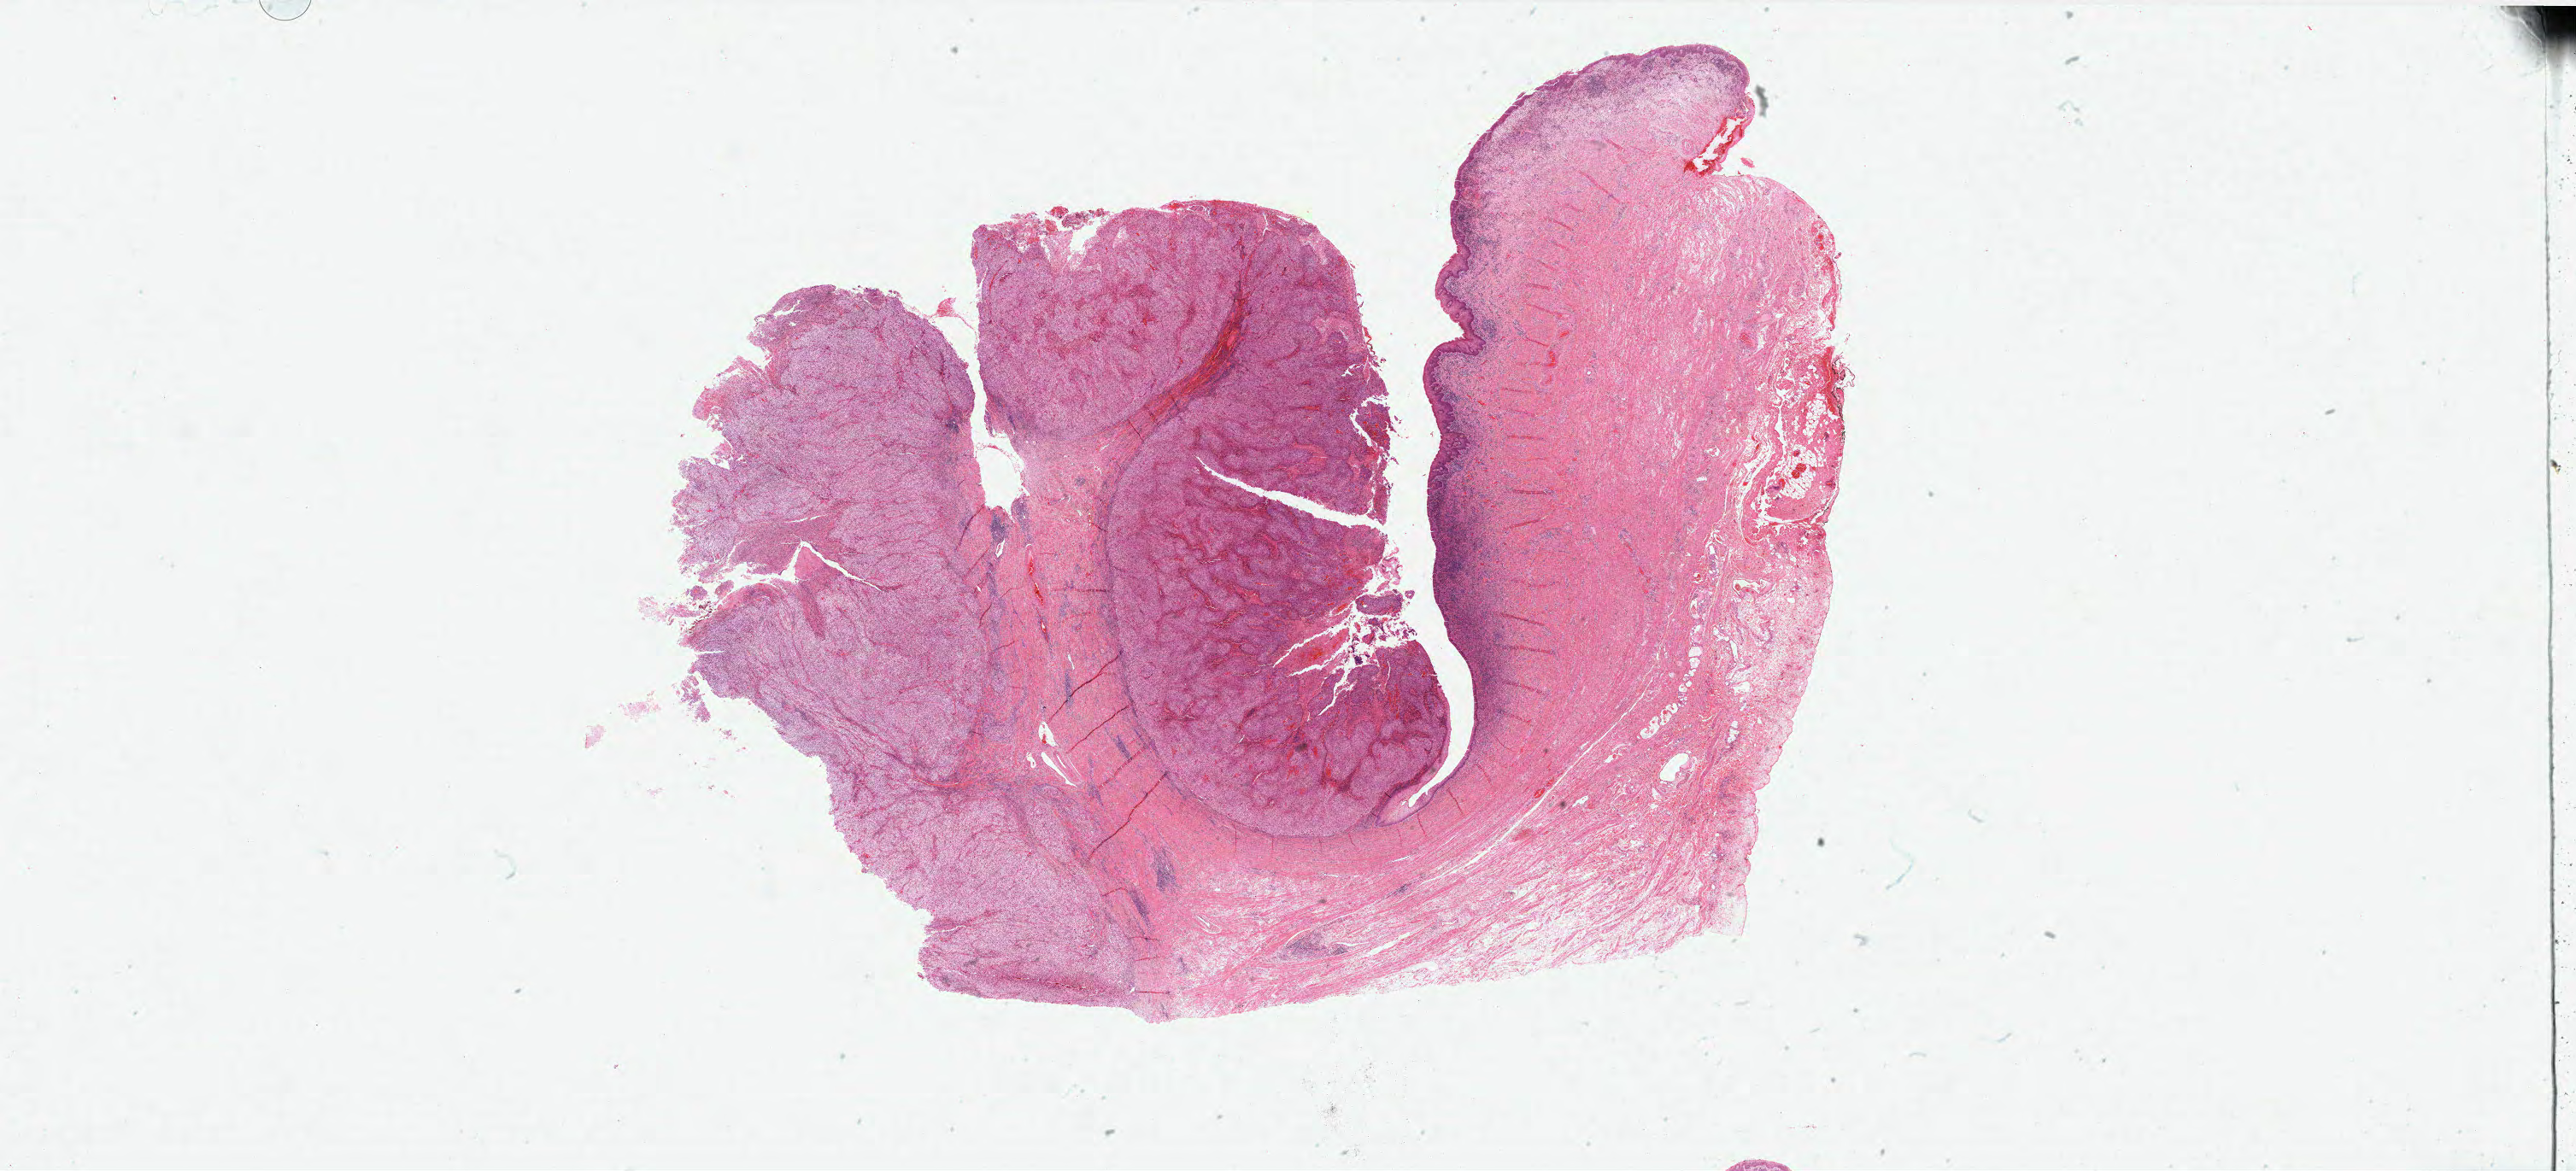
Digitized H&E tissue section (whole slide) — shown as a low-resolution overview of the whole scanned area (about 48.3 x 21.9 mm, acquisition: 40x scan); FFPE section; cervix, primary tumour sample. Patient: female, age at initial diagnosis 25 years. Histologic grade: G2 (moderately differentiated).
FIGO stage: IB. Pathologic diagnosis: Squamous cell carcinoma, keratinizing, NOS (cervix uteri).